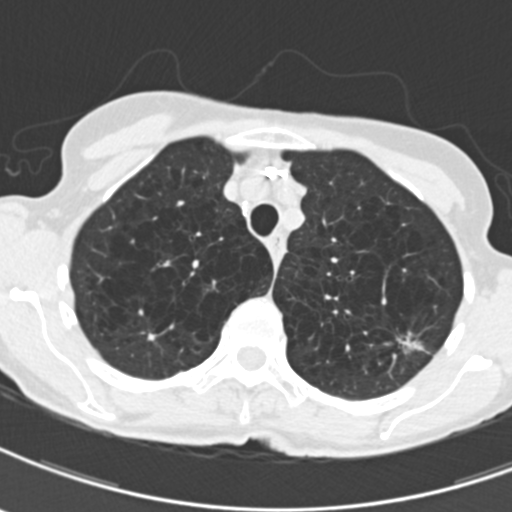
Low-dose screening chest CT, one axial slice; slice 158 of 203 in the series (ordered by position); reconstruction kernel B30f; lung window (W 1500 / L -600 HU); 2 mm slice thickness; 512 × 512 image matrix, field of view 279 × 279 mm.
Outlined on this slice (outlined manually by an expert reader):
- lesion 1 (tumor, upper lobe of left lung): bounding box (x1, y1, x2, y2) in pixels: (398, 334, 427, 355)